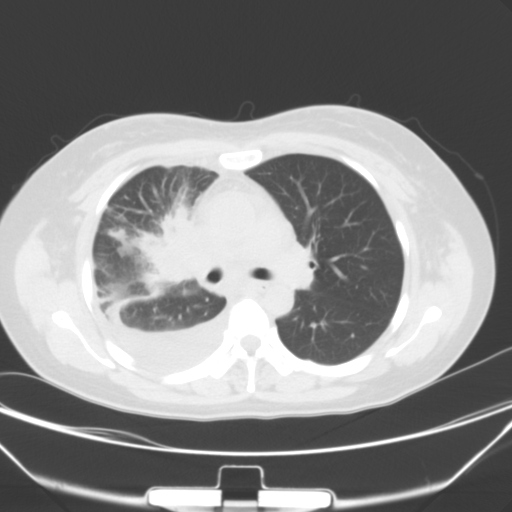
Chest CT, one axial slice. Slice 21 of 40 in the series (ordered by position). 120 kVp. Lung window (W 1500 / L -600 HU). 512 × 512 image matrix, field of view 352 × 352 mm. Female patient, age 36 years. Case-level facts recorded for this patient, not image findings: clinical TNM (as recorded): T1b N2 M0; histopathological grade: G3.
Annotated regions visible in this slice (bounding box drawn by a radiologist):
- lung tumour (recorded histology: adenocarcinoma): bounding box (x1, y1, x2, y2) in pixels: (140, 208, 210, 290)